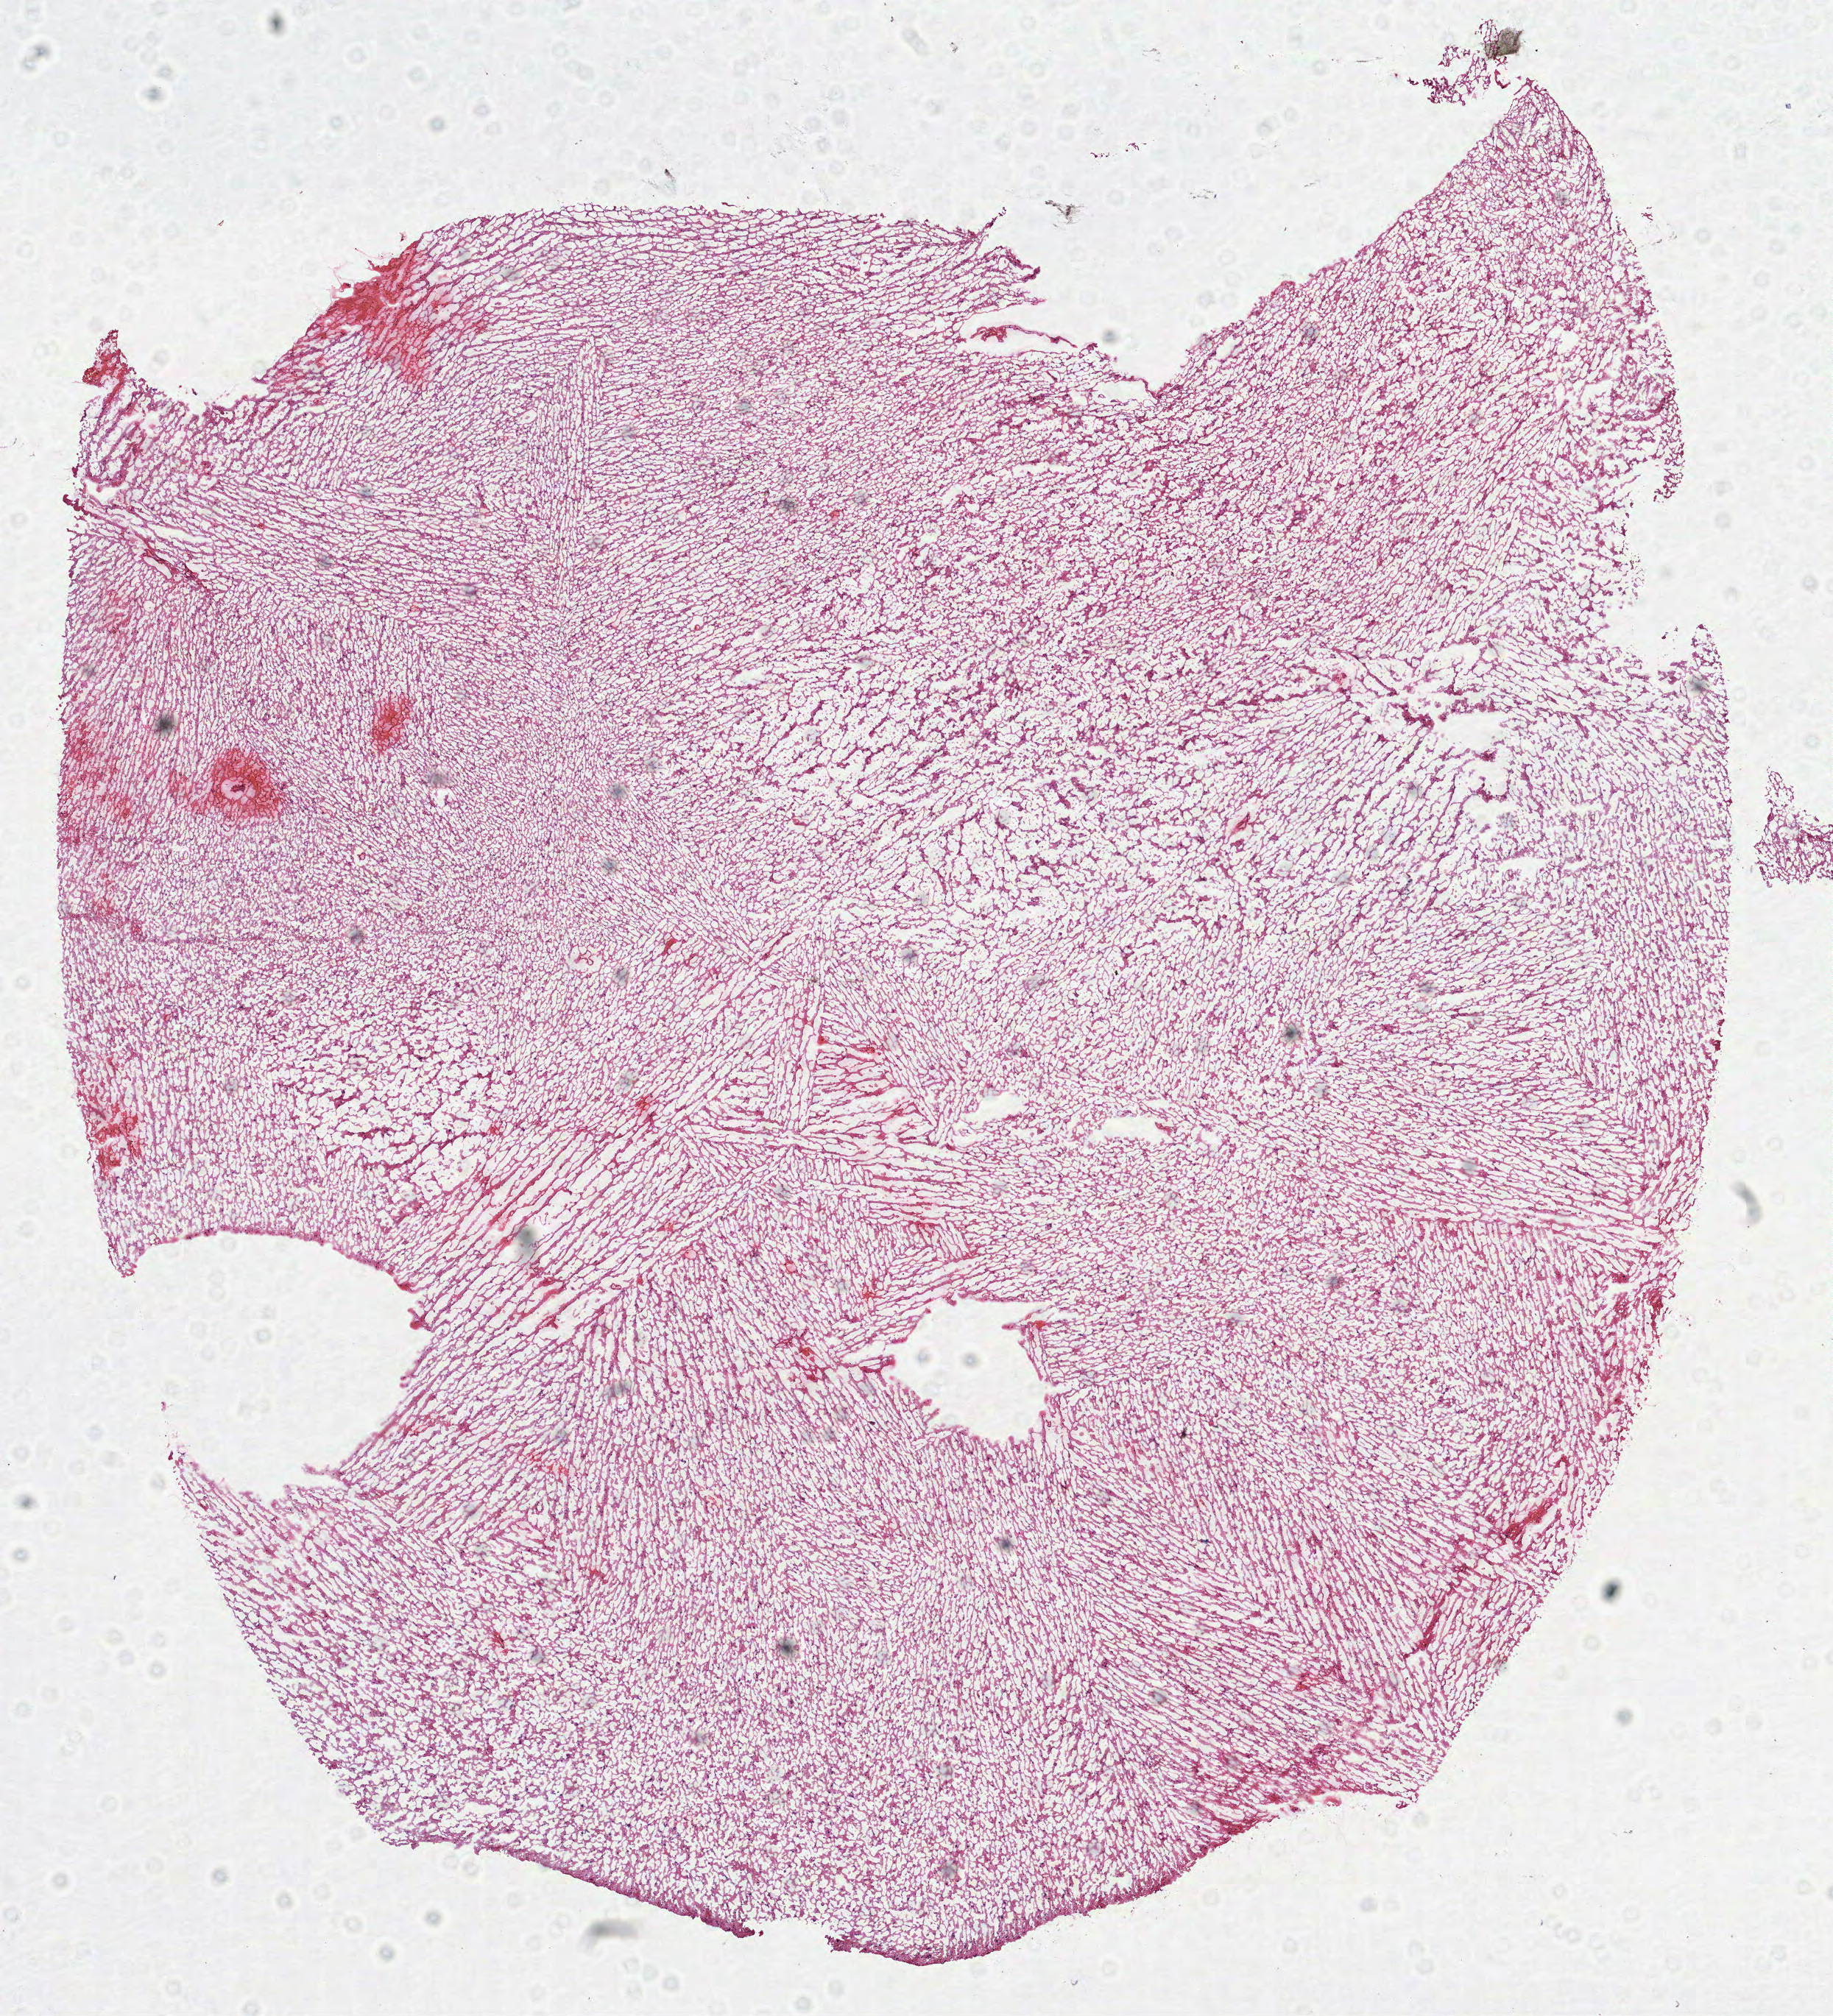
Digitized Hematoxylin and eosin (H&E) stained tissue section (whole slide) — low-resolution overview of the scanned area, about 10.0 x 11.0 mm (from a 40x scan). Frozen section from the top of the tissue portion. Sample: primary tumour, brain. Male patient; age at initial diagnosis 43 years. Histologic grade: G3 (poorly differentiated). Slide review estimates, as recorded: tumour cells 100%, tumour nuclei 70%, normal cells 0%, stromal cells 0%, necrosis 0%.
Diagnosis: Oligodendroglioma, anaplastic.